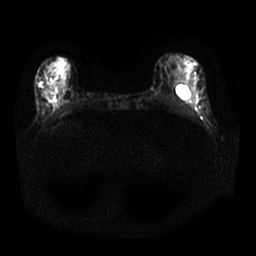
Breast MRI, one axial slice. Slice 9 of 25 in the series (ordered by position). Diffusion-weighted series; image 2 of 4 stored at this slice position (different b-values; order by instance number). 1.5 T. 256 × 256 image matrix, field of view 340 × 340 mm. Female patient.
Structures marked on this image (manually delineated by an expert):
- tumour on diffusion-weighted imaging: bounding box [x1, y1, x2, y2] px = [39, 82, 42, 87]